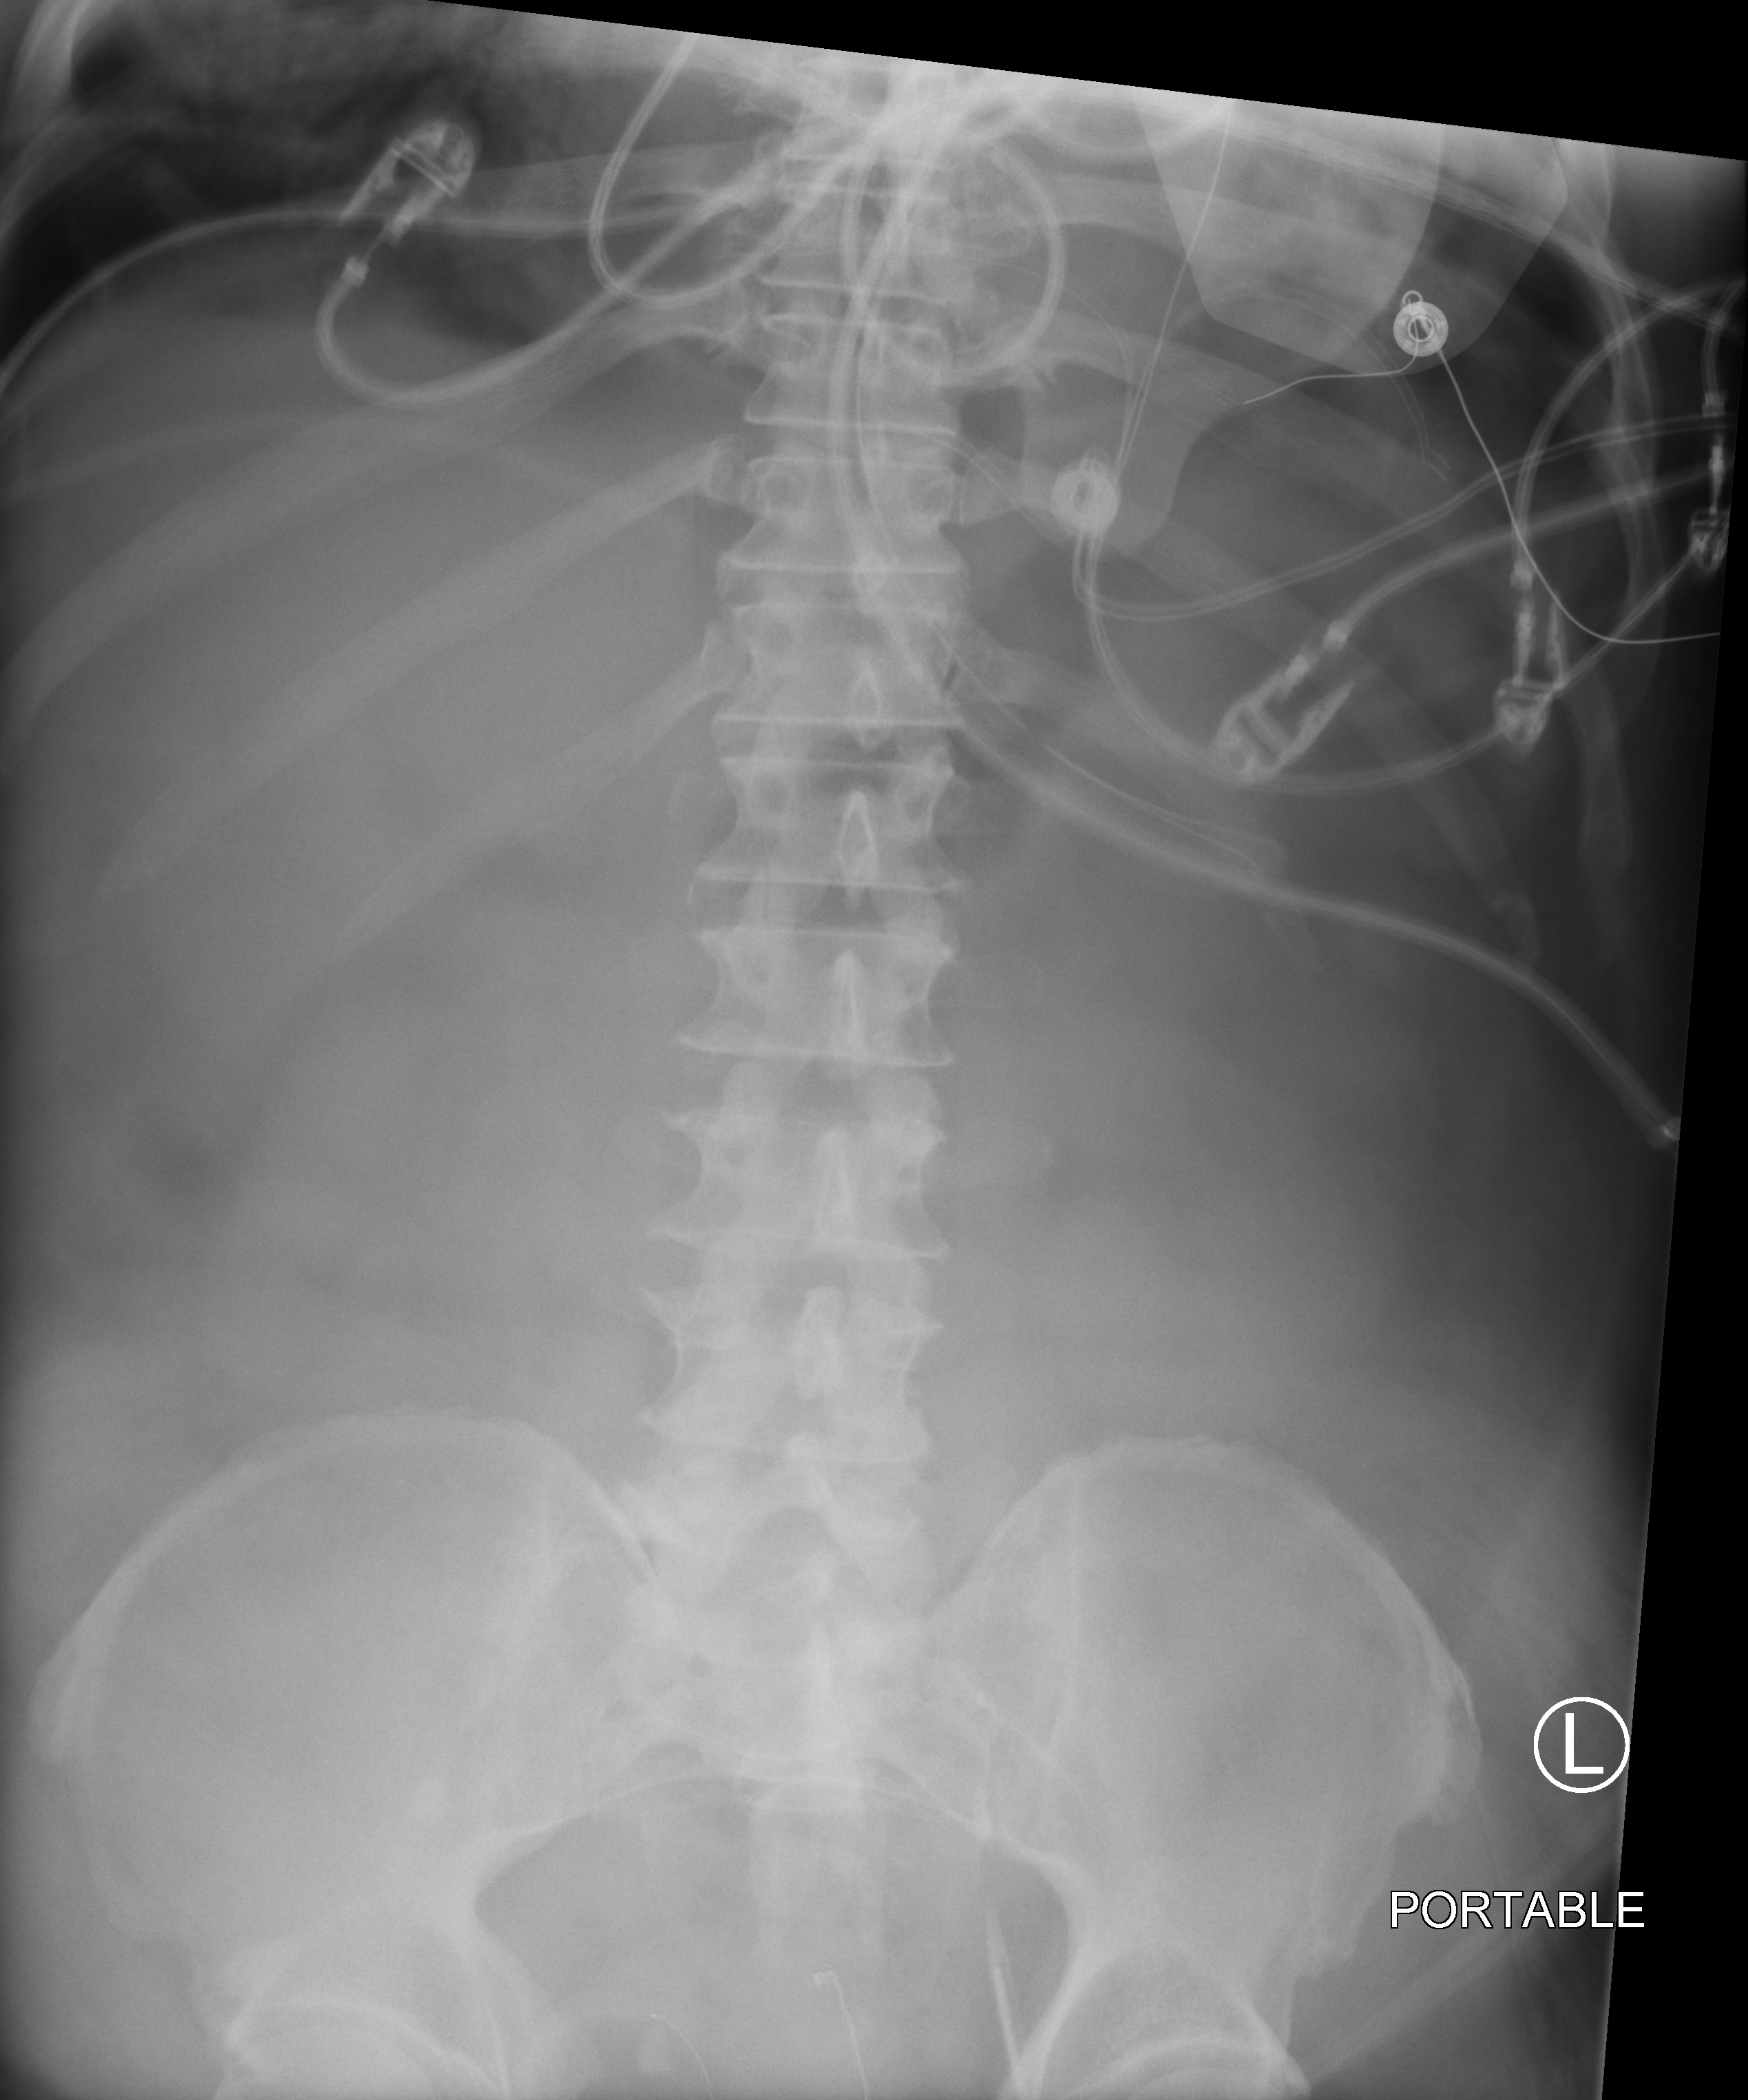
Portable abdomen radiograph; anteroposterior (AP) projection. Patient hospitalised with COVID-19; male, aged 60–74 years.
Admission-level facts for this patient (not findings on this image; timing relative to this image not recorded): mechanically ventilated during this hospital stay: yes; hypertension (admission record): yes.